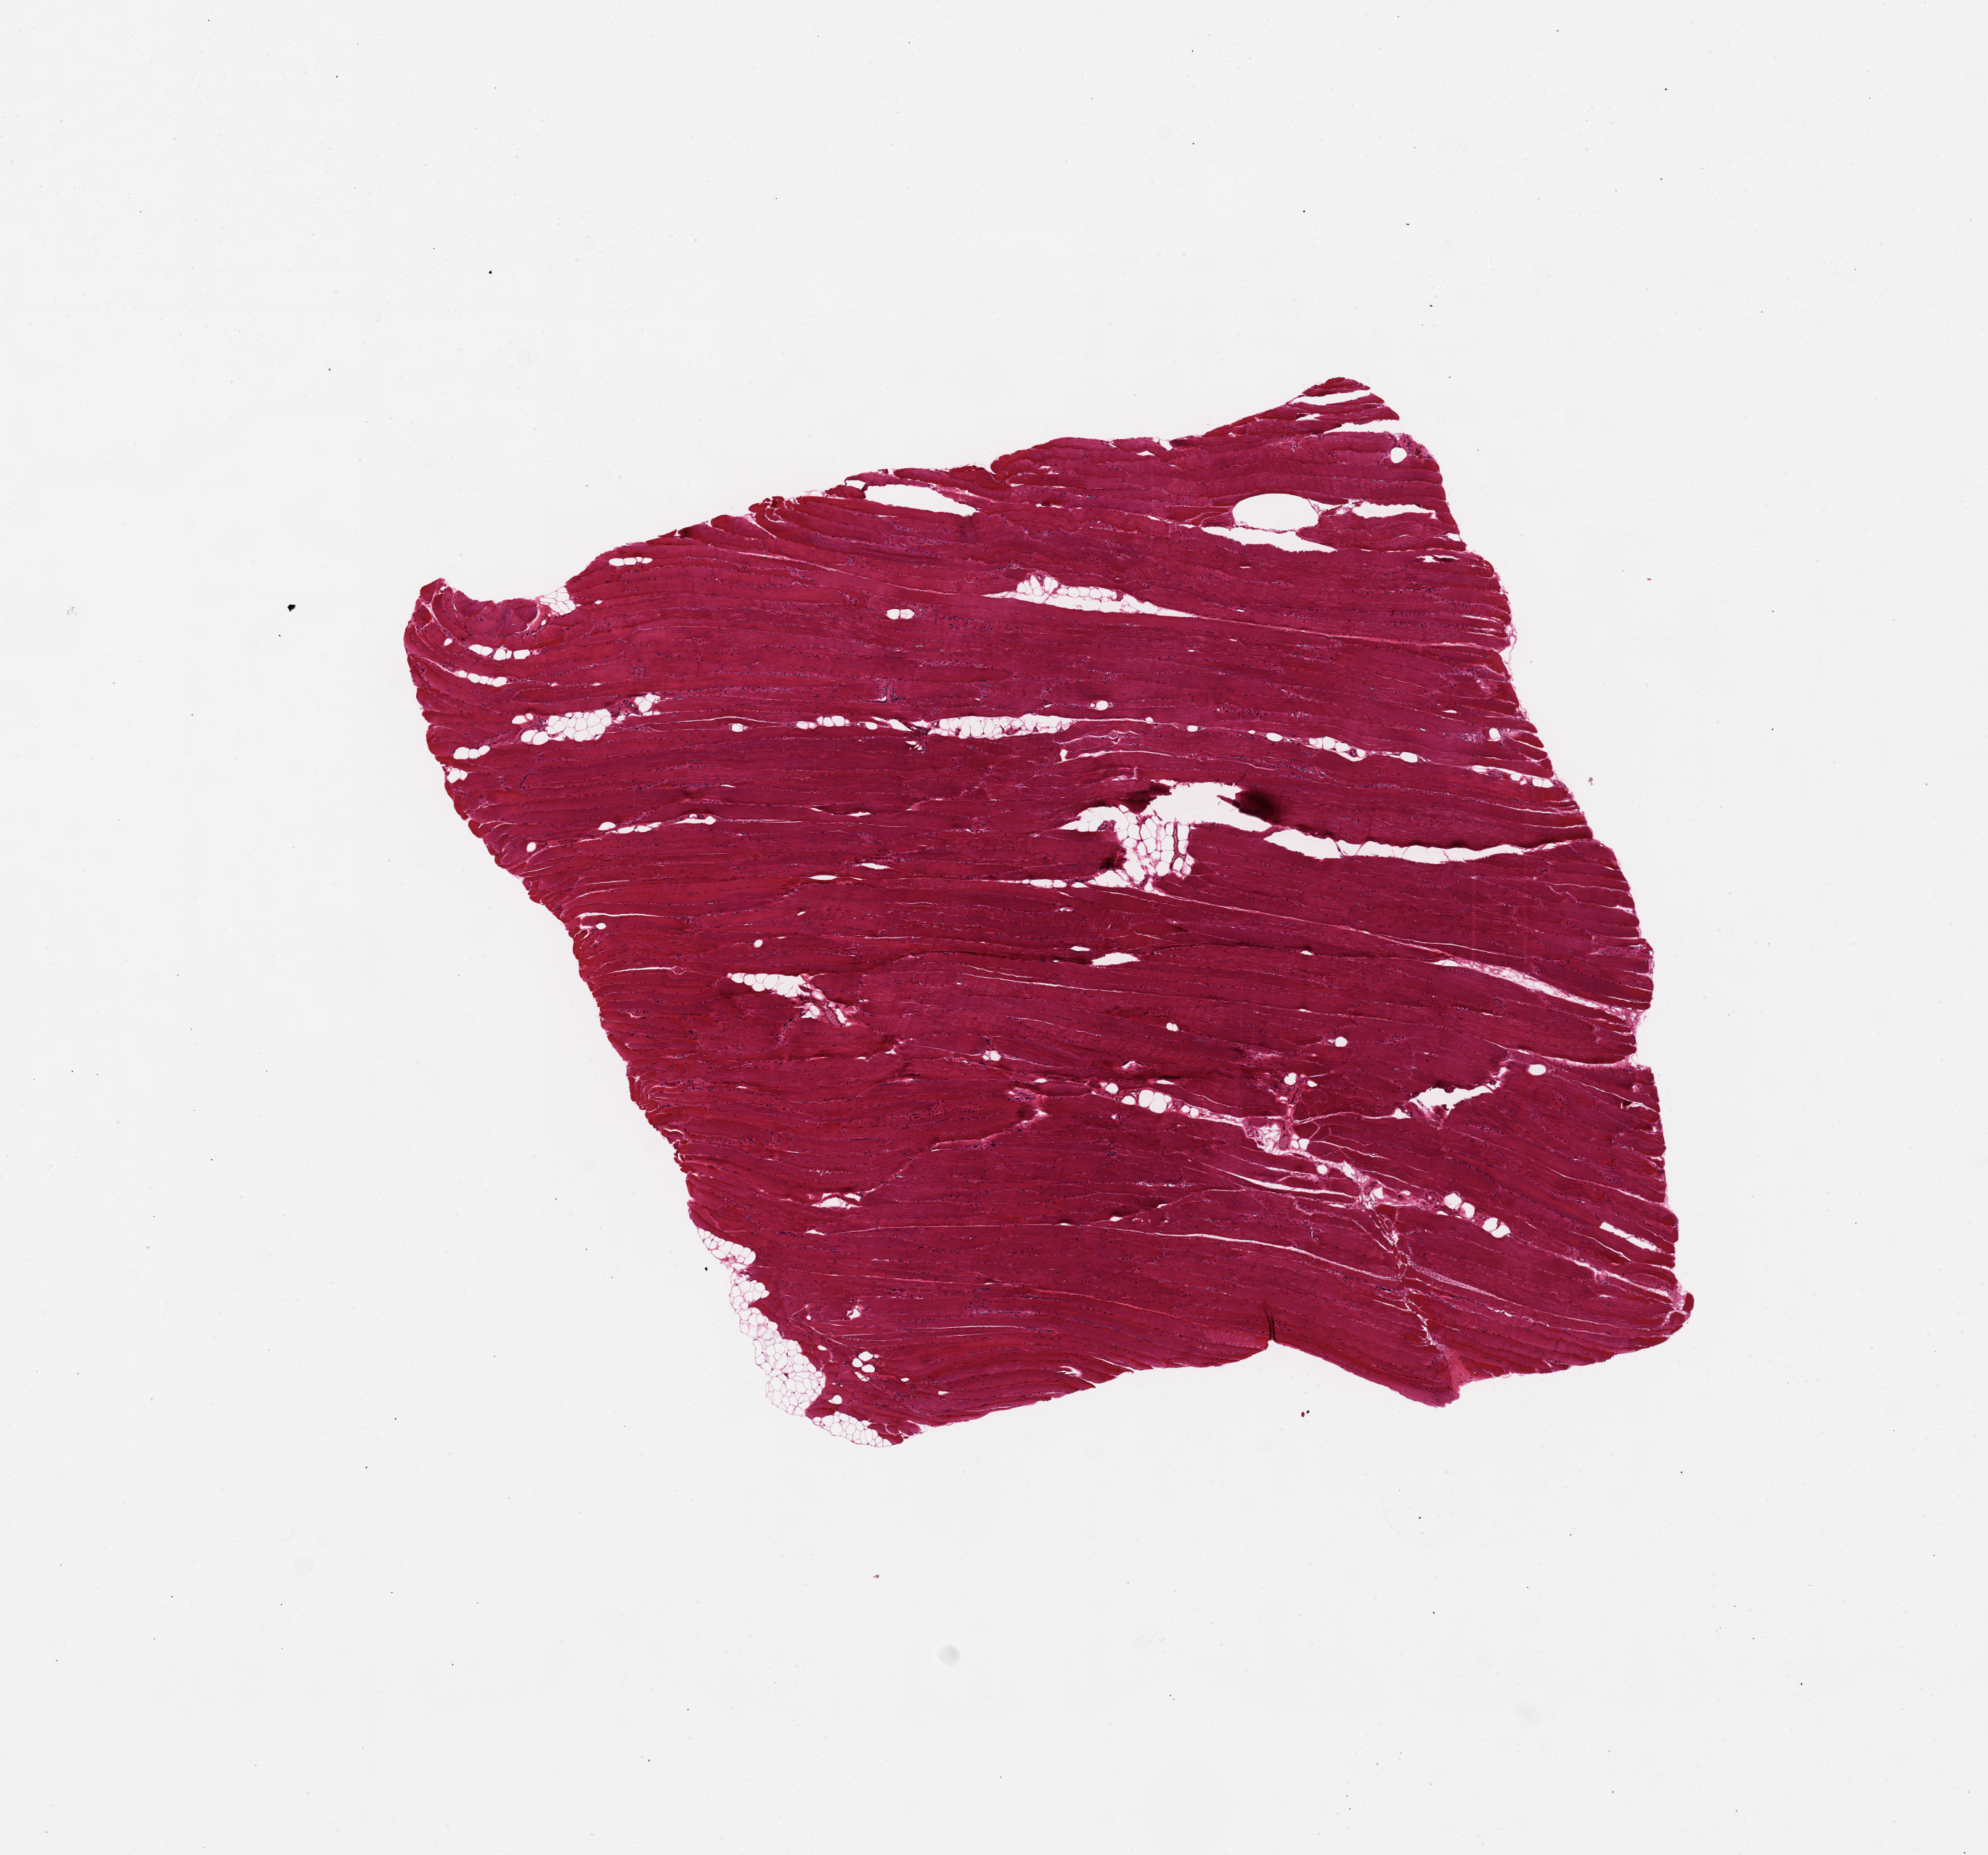
Whole-slide image, haematoxylin and eosin stain, brightfield, low-resolution overview of the scanned area, about 10.8 x 10.1 mm (acquisition: 20x scan); PAXgene-fixed, paraffin-embedded tissue; section of skeletal muscle (target tissue); donor tissue sample. Donor: female.
Reviewer comment on this tissue sample: minimal fat.